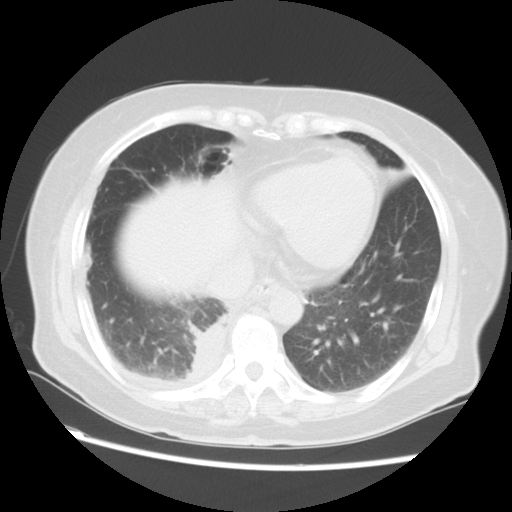
Chest CT, one axial slice; slice 21 of 57 in the series (ordered by position); 120 kVp; lung window (W 1500 / L -600 HU); 5 mm slice thickness; 512 × 512 image matrix, field of view 350 × 350 mm. Female patient, age 69 years. From the clinical record (not read from this slice): clinical TNM (as recorded): T2 N1 M1a.
Outlined on this slice (bounding box drawn by a radiologist):
- lung tumour (recorded histology: adenocarcinoma): box from (x=174, y=318) to (x=228, y=395) px